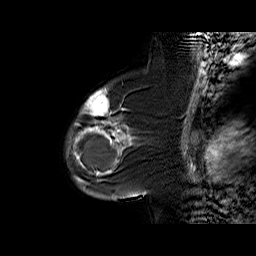
Breast MRI (dynamic contrast-enhanced), one sagittal slice; slice 44 of 60 in the series (ordered by position); dynamic contrast-enhanced series, time point 2 of 6 at this slice position (early post-contrast); 1.5 T; TE 6.3 ms, TR 32.4 ms; 4 mm slice thickness; 256 × 256 image matrix. Female patient. Case-level facts recorded for this patient, not image findings: setting: breast cancer imaged before/during neoadjuvant chemotherapy; receptor status: triple-negative.
Outlined on this slice (semi-automatic segmentation, software-assisted and operator-edited):
- analysis volume of interest (the breast-tissue region the enhancement analysis was run in; not a lesion): bounding box <65,88,137,187> (left, top, right, bottom; pixels)
- tumour enhancement mask (voxels above the 100 % enhancement threshold inside the analysis volume of interest): <72,88,131,175>